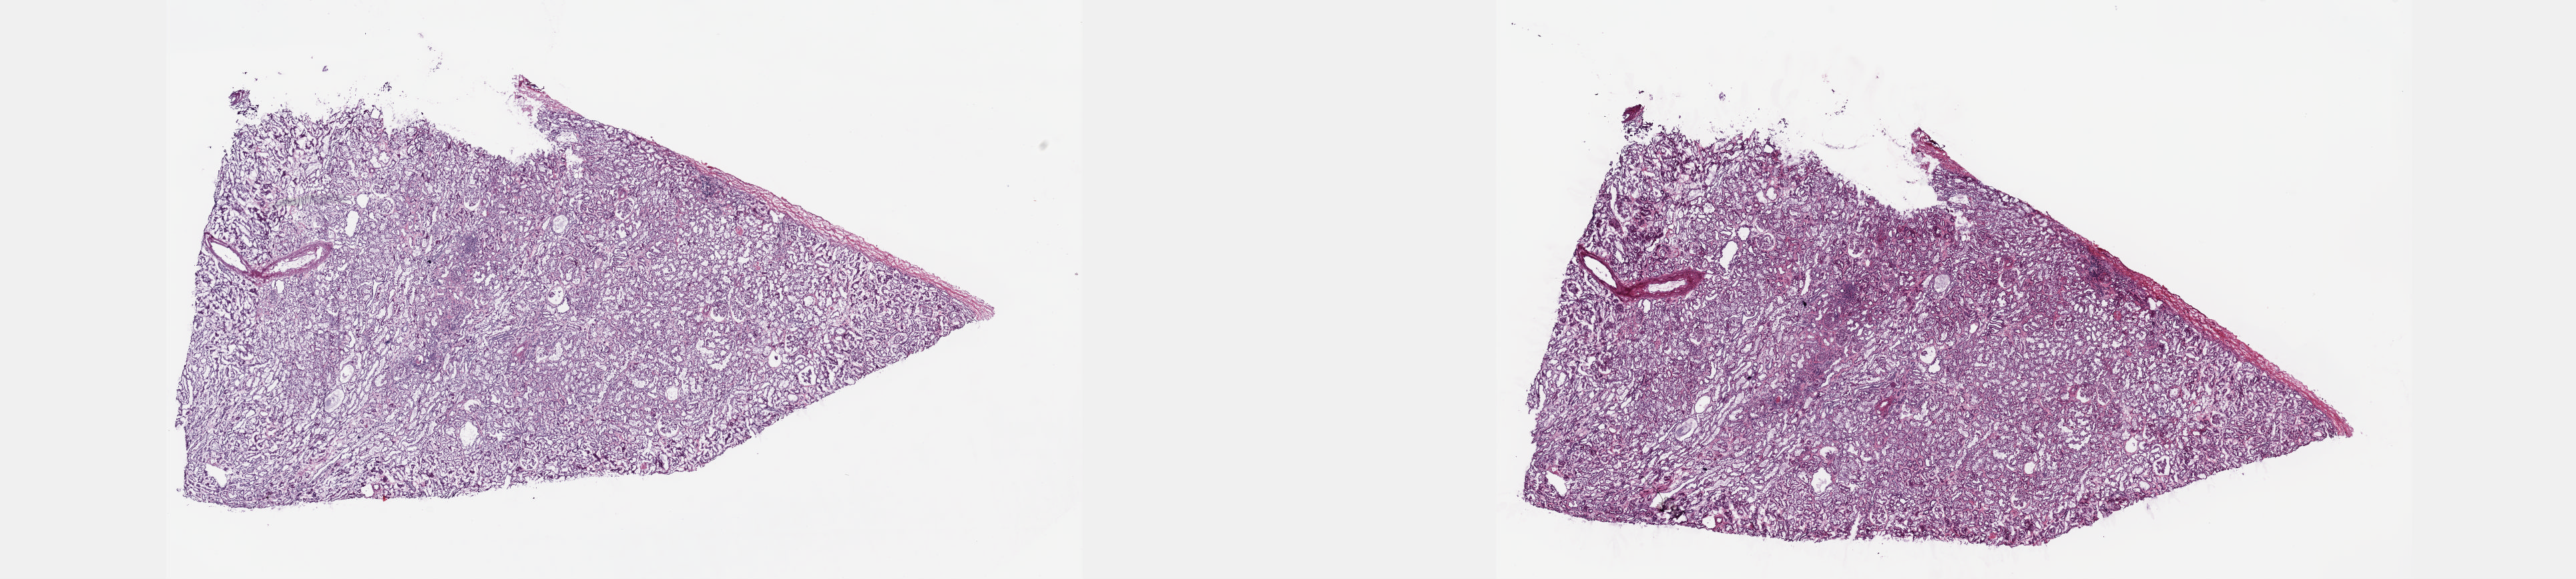
Digitized Hematoxylin and eosin (H&E) stained tissue section (whole slide) — whole scanned area (about 31.1 x 7.0 mm, acquisition: 20x scan) shown as a low-resolution overview, frozen section from the top of the tissue portion, sample: solid tissue normal (non-tumour tissue), retroperitoneum and peritoneum. Female patient. Pathologist review of this section (percent, as recorded): tumour cells 0%, tumour nuclei 0%, normal cells 100%, stromal cells 0%, necrosis 0%. Infiltration values recorded for this section: lymphocyte infiltration 0%, monocyte infiltration 0%, neutrophil infiltration 0%.
This section: solid tissue normal (non-tumour) sample from the same patient. Patient diagnosis: Leiomyosarcoma, NOS (retroperitoneum).